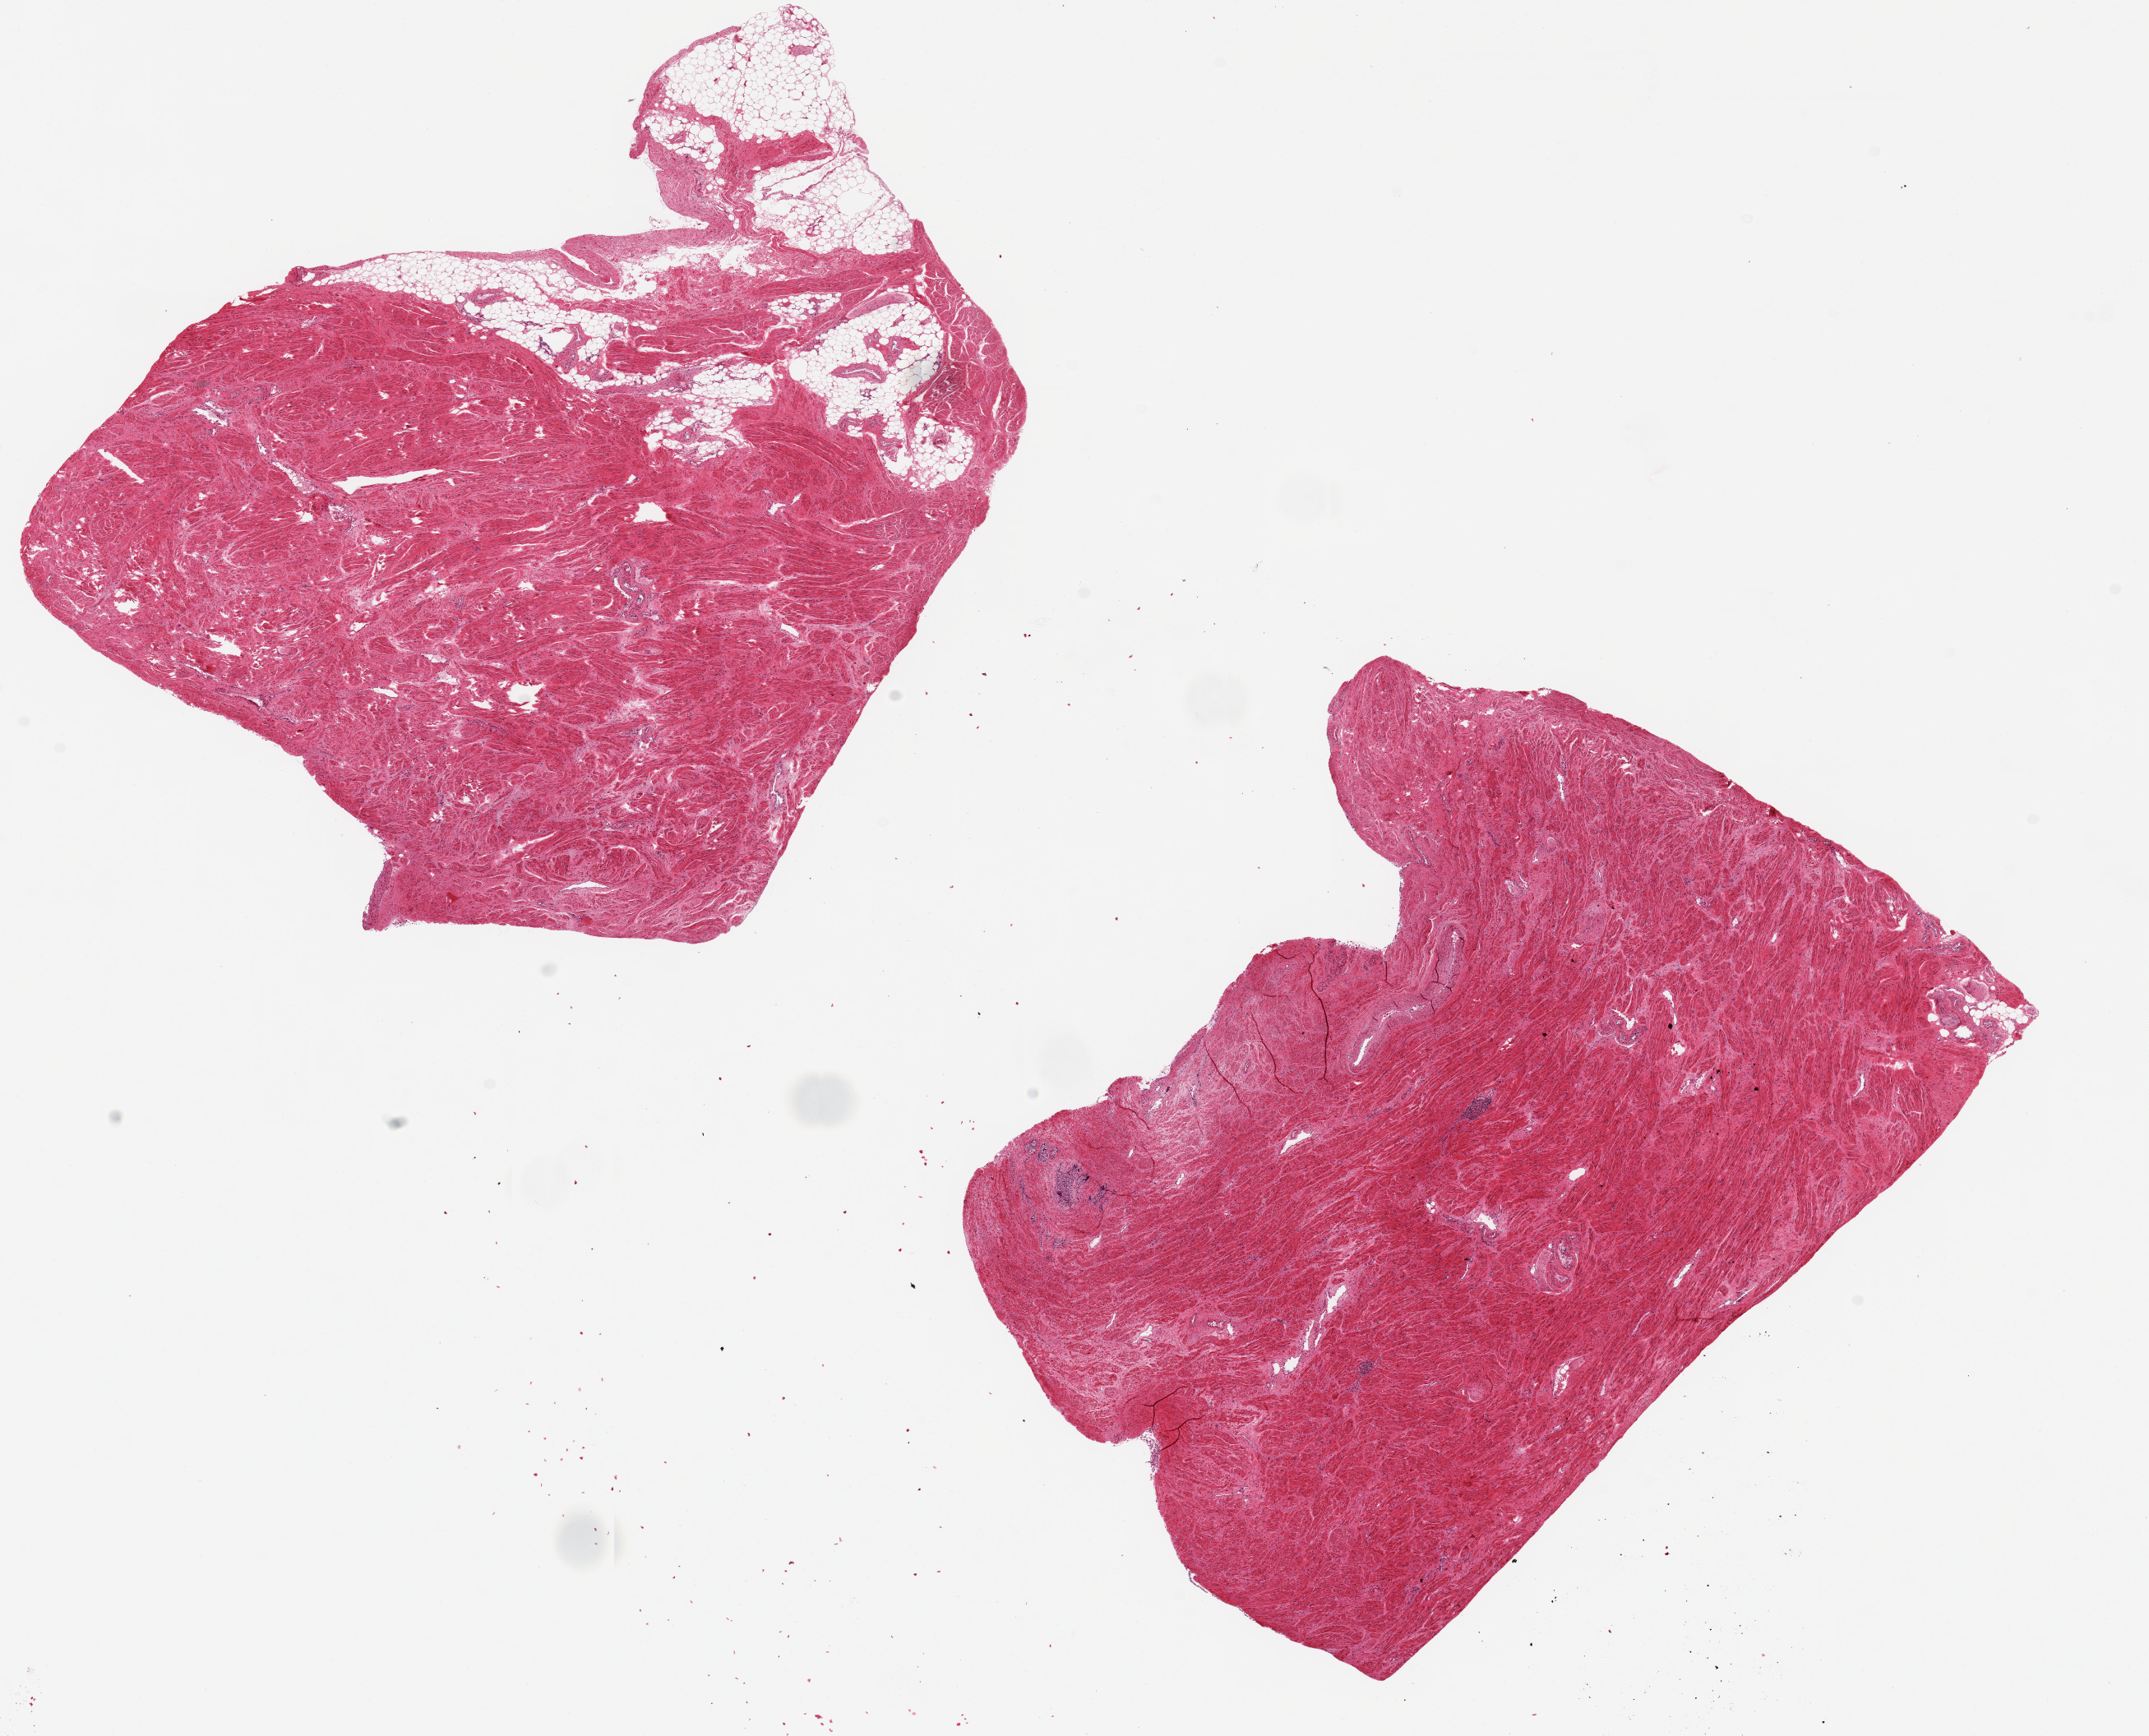
Hematoxylin and eosin (H&E) whole-slide image, a low-resolution overview of the entire scanned area, about 20.7 x 16.7 mm, PAXgene-fixed, paraffin-embedded tissue, section of prostate (target tissue), donor tissue sample. Donor sex: male.
Review note (as recorded): 2 pieces, 10x9 & 9x7mm; except for ~5% autolyzed glands, tissue is muscular; 30% adipose in 1 piece; glands = 3, muscle = 1 (autolysis).